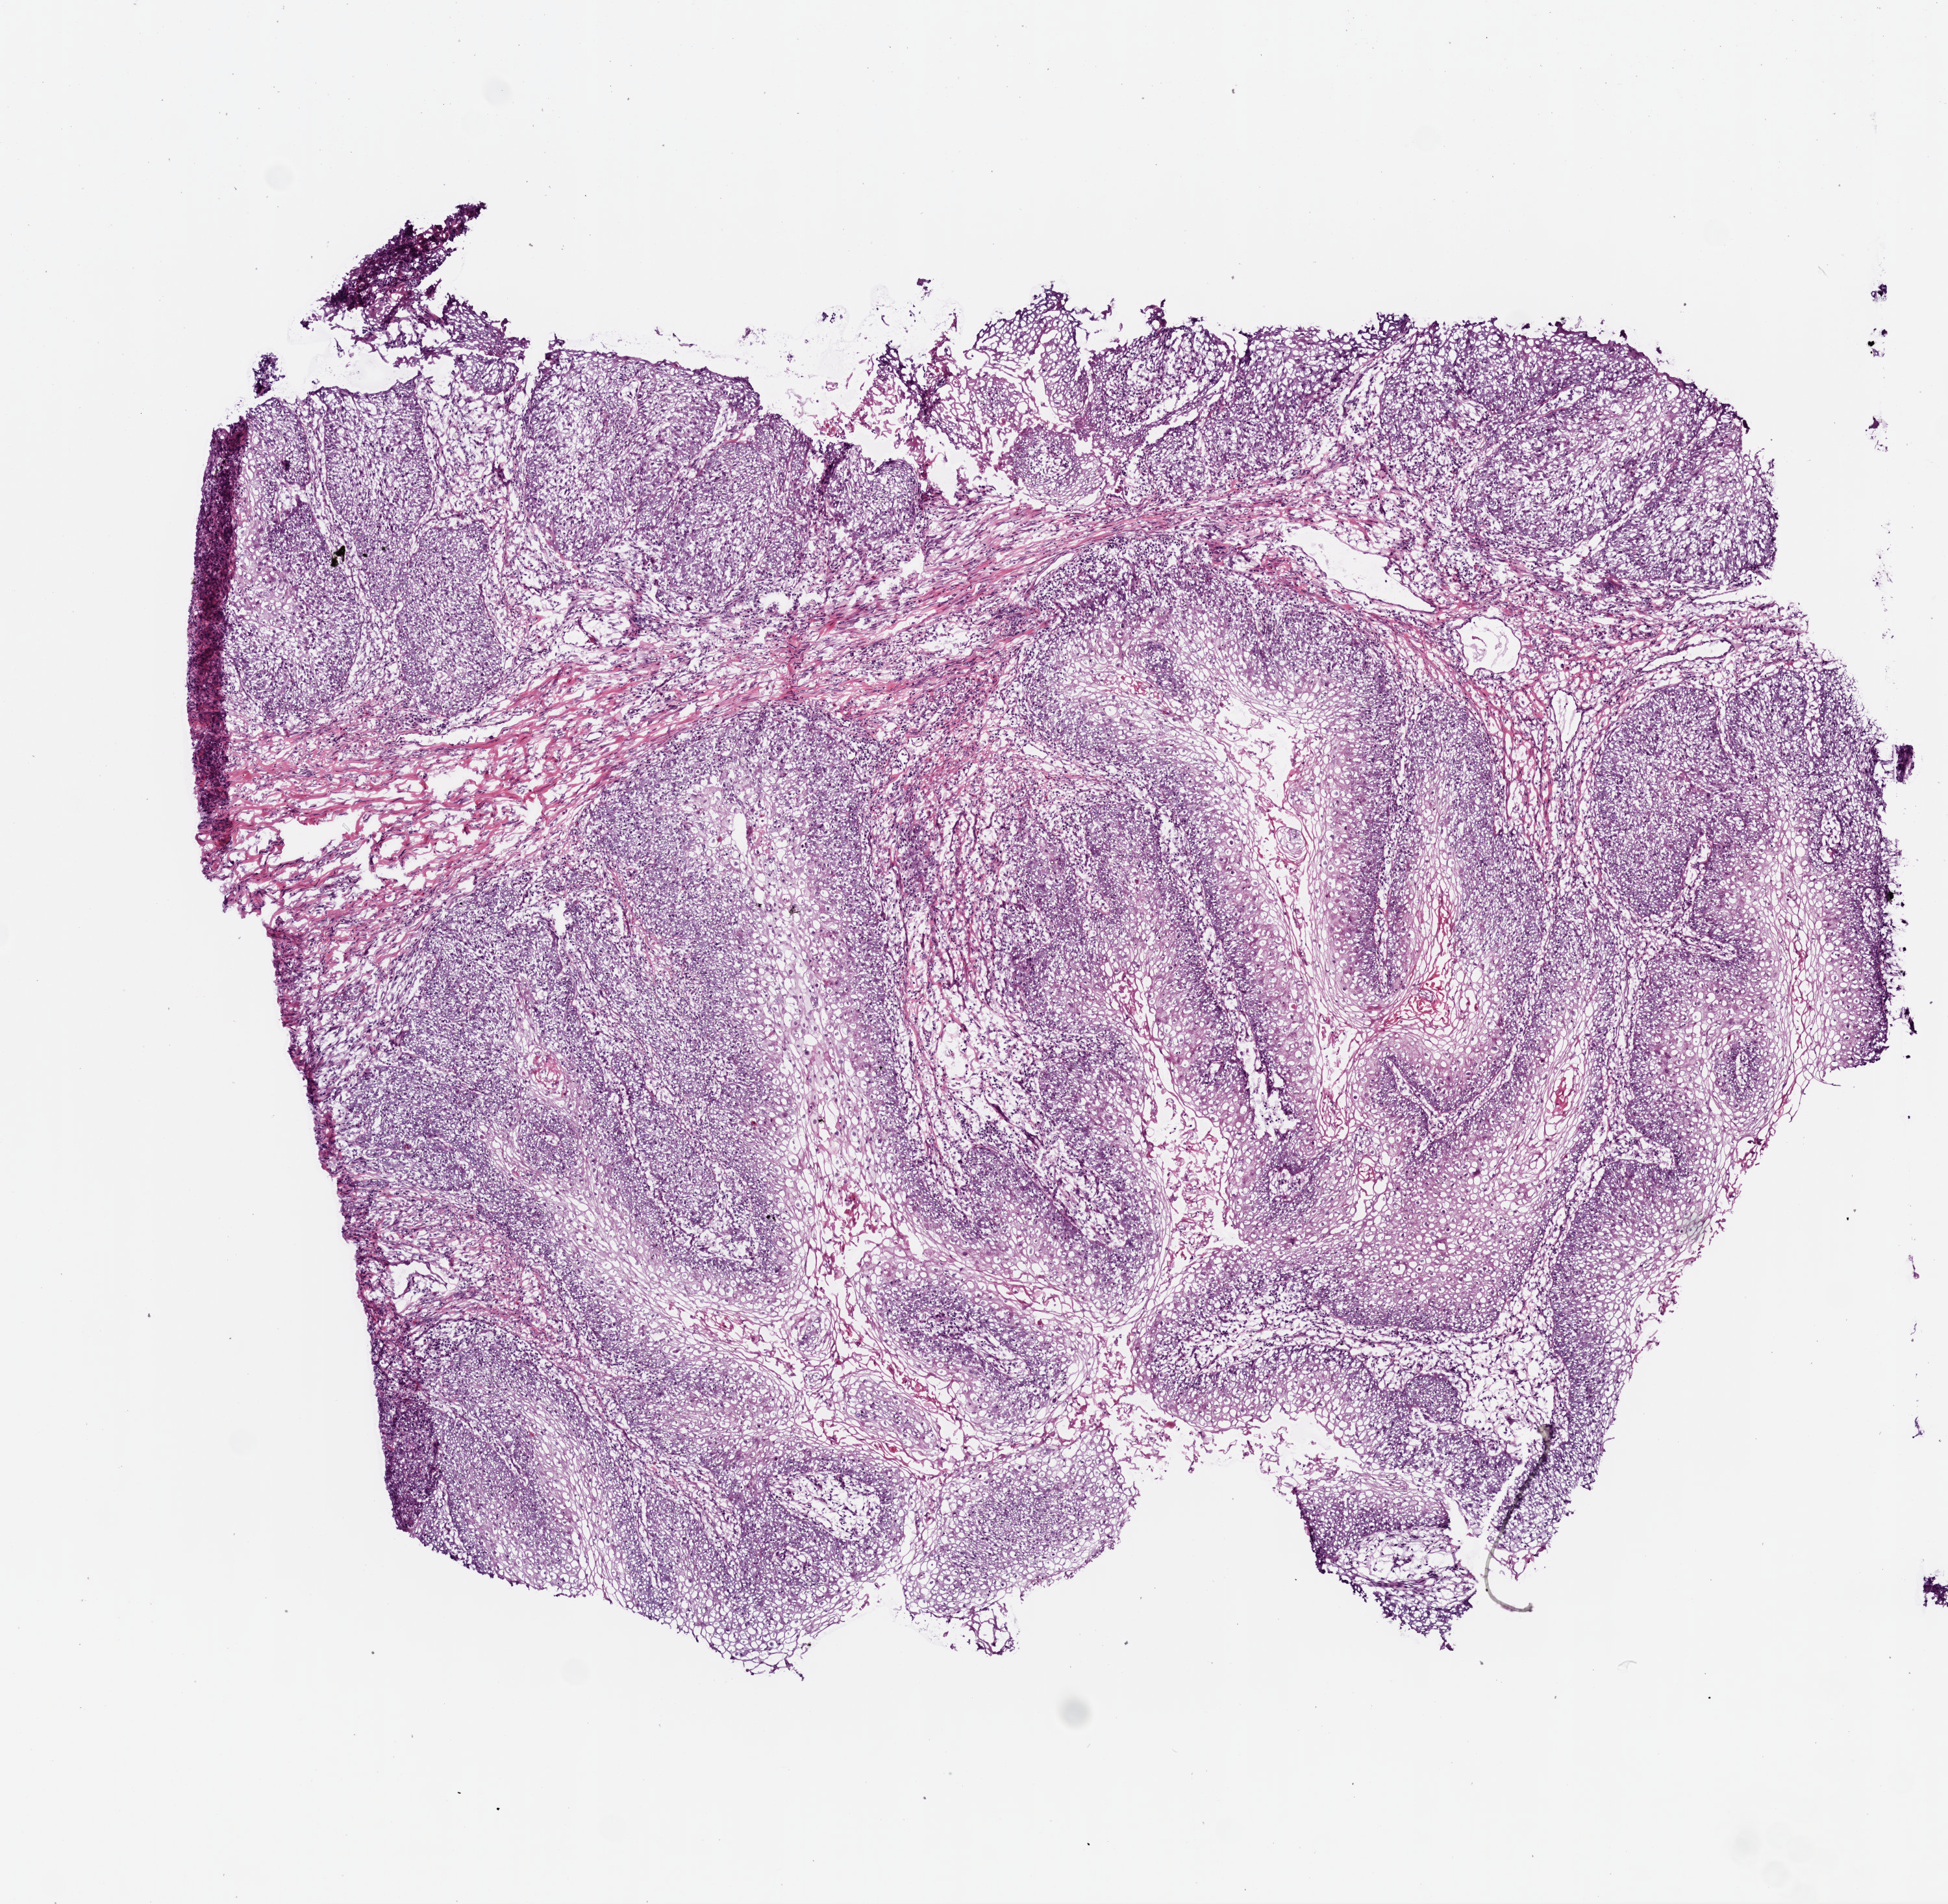
Whole-slide histology image, H&E-stained, whole scanned area (about 6.0 x 5.9 mm) shown as a low-resolution overview. Frozen section from the bottom of the tissue portion. Head and neck, primary tumour sample. Male, age 87 years at initial diagnosis. Histologic grade: G2 (moderately differentiated). Slide review estimates, as recorded: tumour cells 96%, tumour nuclei 80%, stromal cells 4%, necrosis 0%. Inflammatory infiltration, as recorded: lymphocyte infiltration 10%.
Diagnosis: Squamous cell carcinoma, NOS (cheek mucosa). AJCC pathologic stage: IVA (6th edition). Lymph nodes positive (case pathology): 6 of 46 examined.